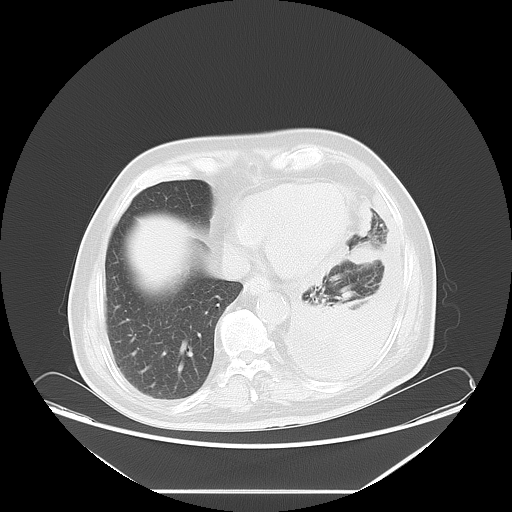
Chest CT, one axial slice; position 20 of 63 along the scan axis; 120 kVp; lung window (W 1500 / L -600 HU); 512 × 512 image matrix, field of view 448 × 448 mm. Male patient, age 67 years. Case-level facts recorded for this patient, not image findings: clinical TNM (as recorded): T1b N1 M1a; histopathological grade: G3.
Annotated regions visible in this slice (bounding box drawn by a radiologist):
- lung tumour (recorded histology: small cell carcinoma): box from (x=348, y=238) to (x=384, y=268) px